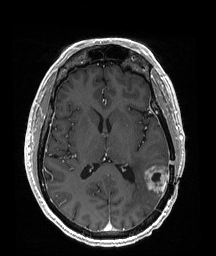
Brain MRI from a brain-tumour surgery series, one axial slice; slice 90 of 192 in the series (ordered by position); T1-weighted post-contrast; 216 × 256 image matrix. Case-level facts recorded for this patient, not image findings: histopathology: Glioblastoma; WHO grade: 4; IDH mutation: no; tumour location: Left Temporoparietal.
Structures marked on this image (manually delineated by an expert):
- tumour: bounding box (x1, y1, x2, y2) in pixels: (144, 166, 170, 197)